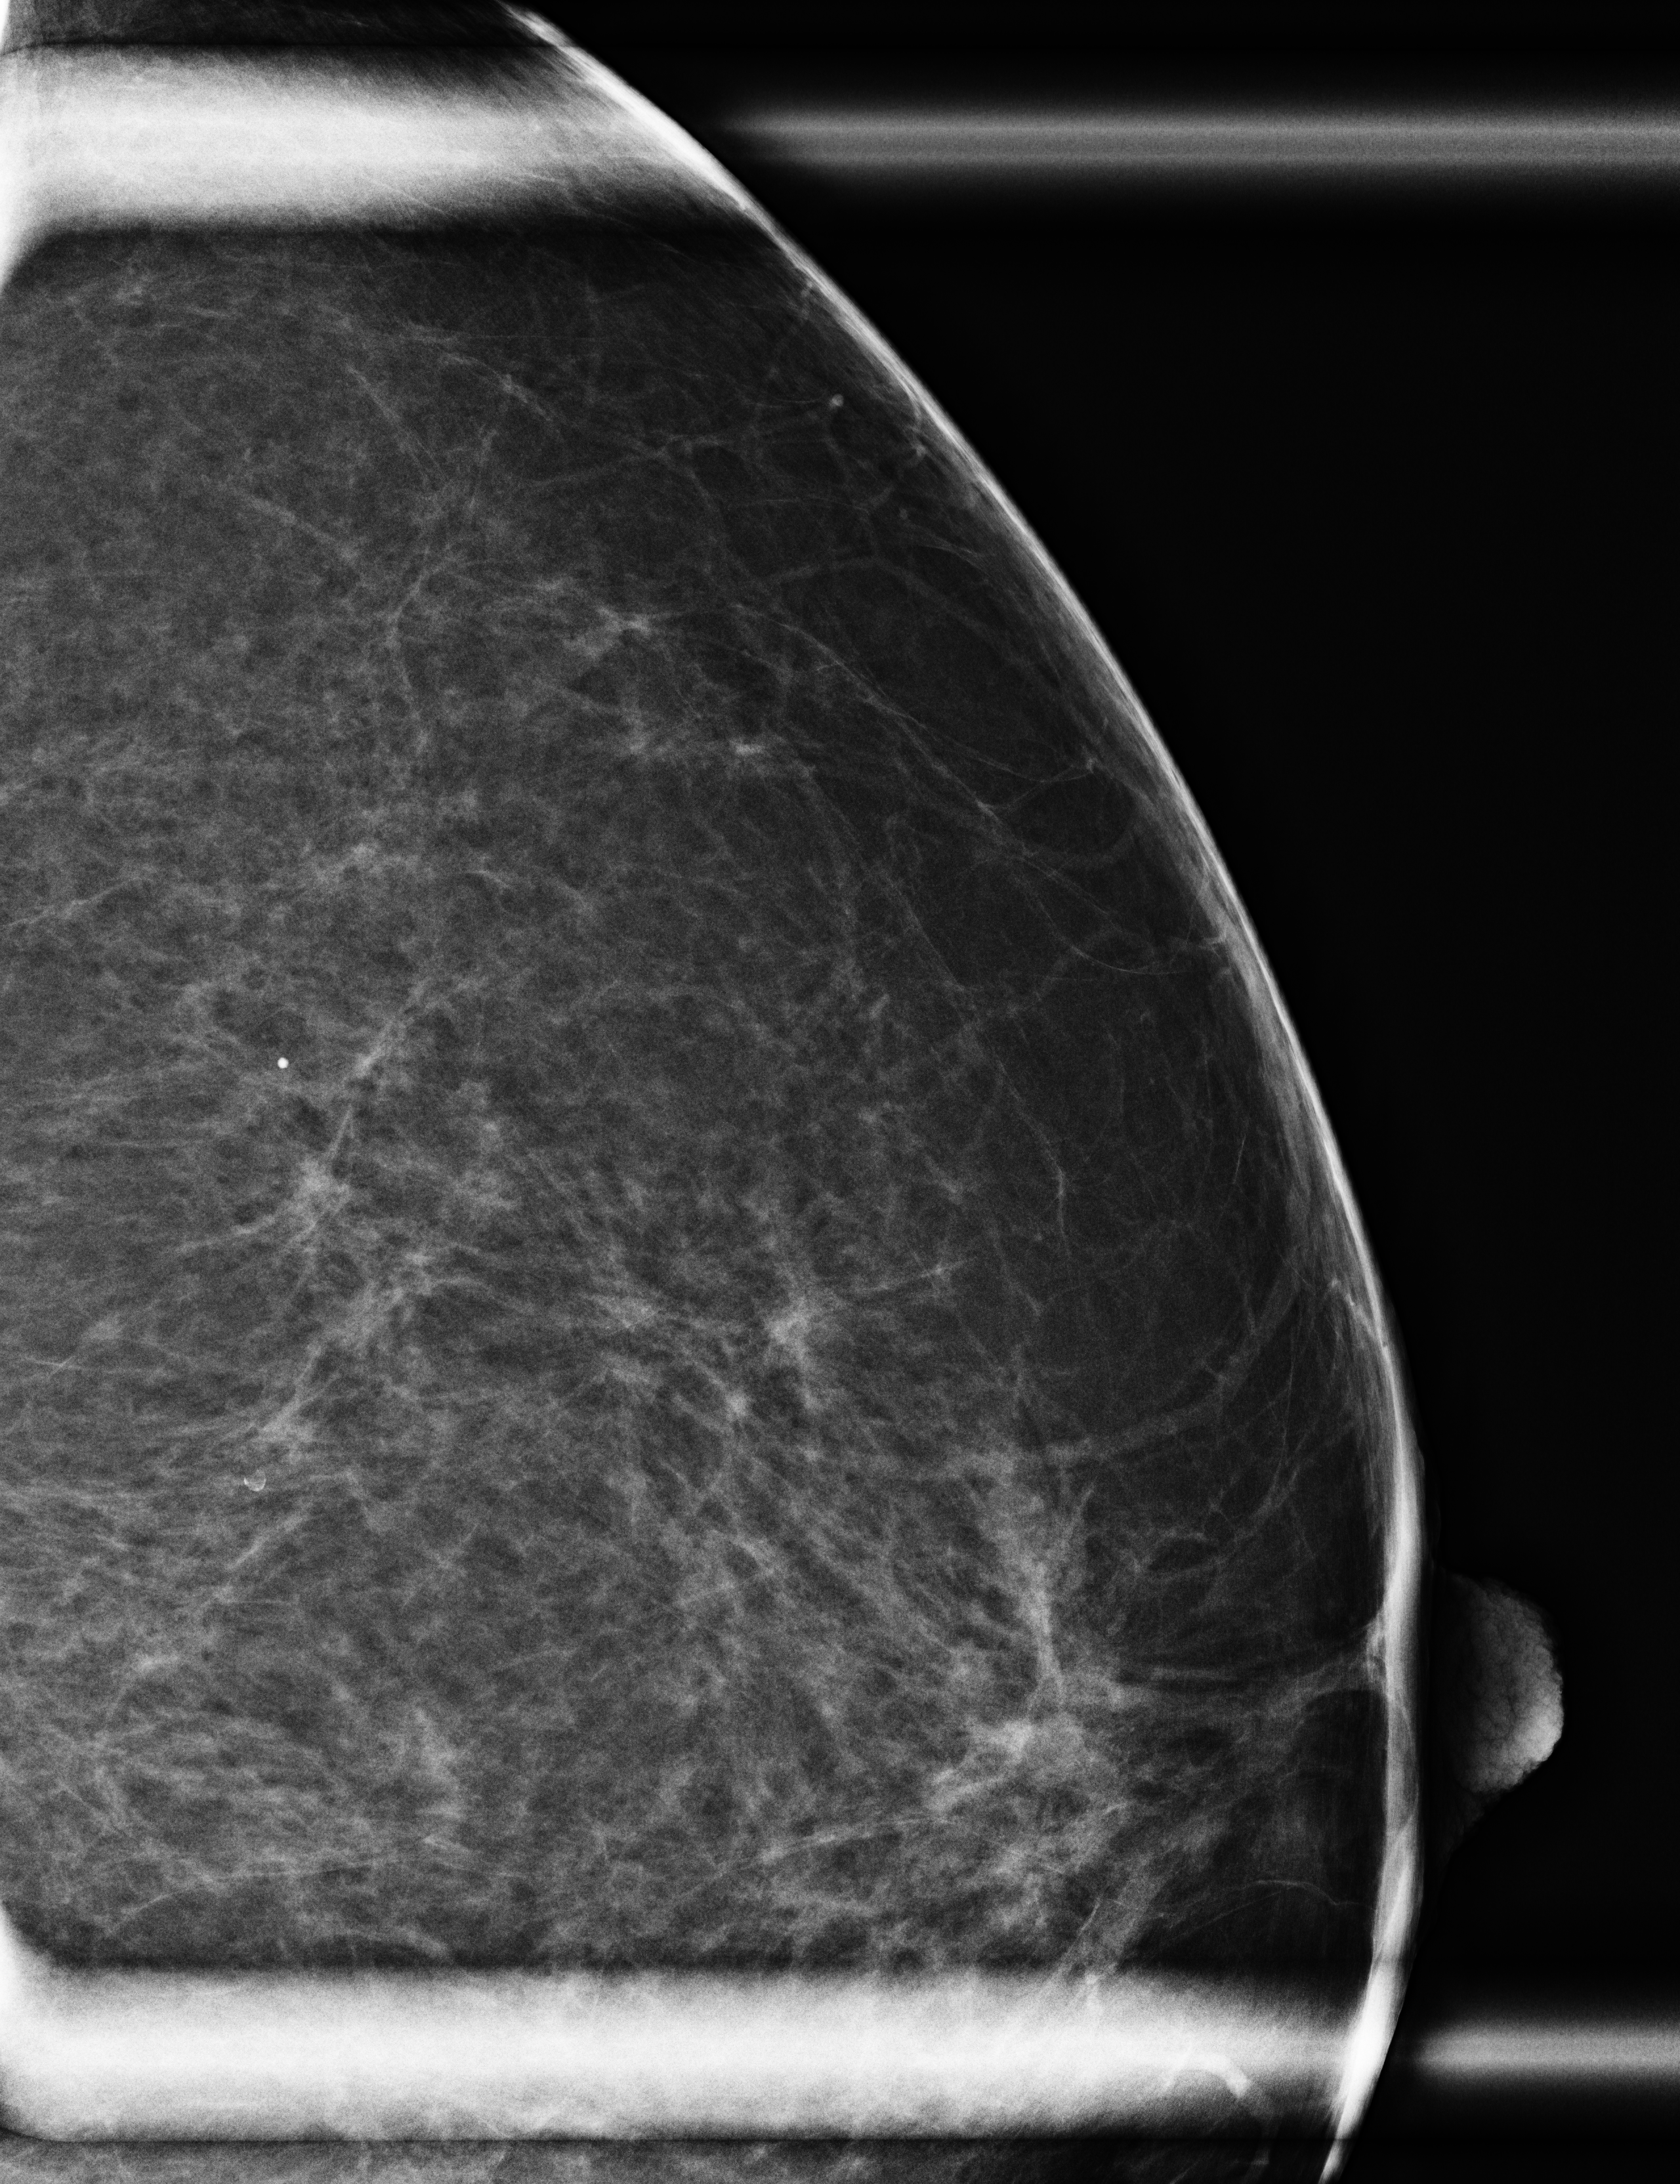
Full-field digital mammogram (FFDM), left breast, craniocaudal (CC) view (magnification), additional (diagnostic) view. Female patient, age 74 years.
- breast density at the screening exam (both breasts): heterogeneously dense (BI-RADS density category c)
- final BI-RADS category for the screening round (tomosynthesis exam, both breasts): category 4
- recall: recalled for additional imaging after this screen